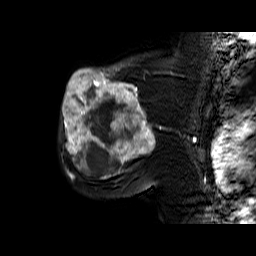
Breast MRI (dynamic contrast-enhanced), one sagittal slice. Position 43 of 60 along the scan axis. Dynamic contrast-enhanced series, time point 2 of 6 at this slice position (early post-contrast). 1.5 T. TE 6.4 ms, TR 32.9 ms. 4 mm slice thickness. 256 × 256 image matrix. Female patient. Case-level facts recorded for this patient, not image findings: setting: breast cancer imaged before/during neoadjuvant chemotherapy; receptor status: triple-negative.
Structures marked on this image (semi-automatically segmented with operator editing):
- analysis volume of interest (the breast-tissue region the enhancement analysis was run in; not a lesion): bounding box <60,65,159,174> (left, top, right, bottom; pixels)
- tumour enhancement mask (voxels above the 100 % enhancement threshold inside the analysis volume of interest): <62,65,156,174>